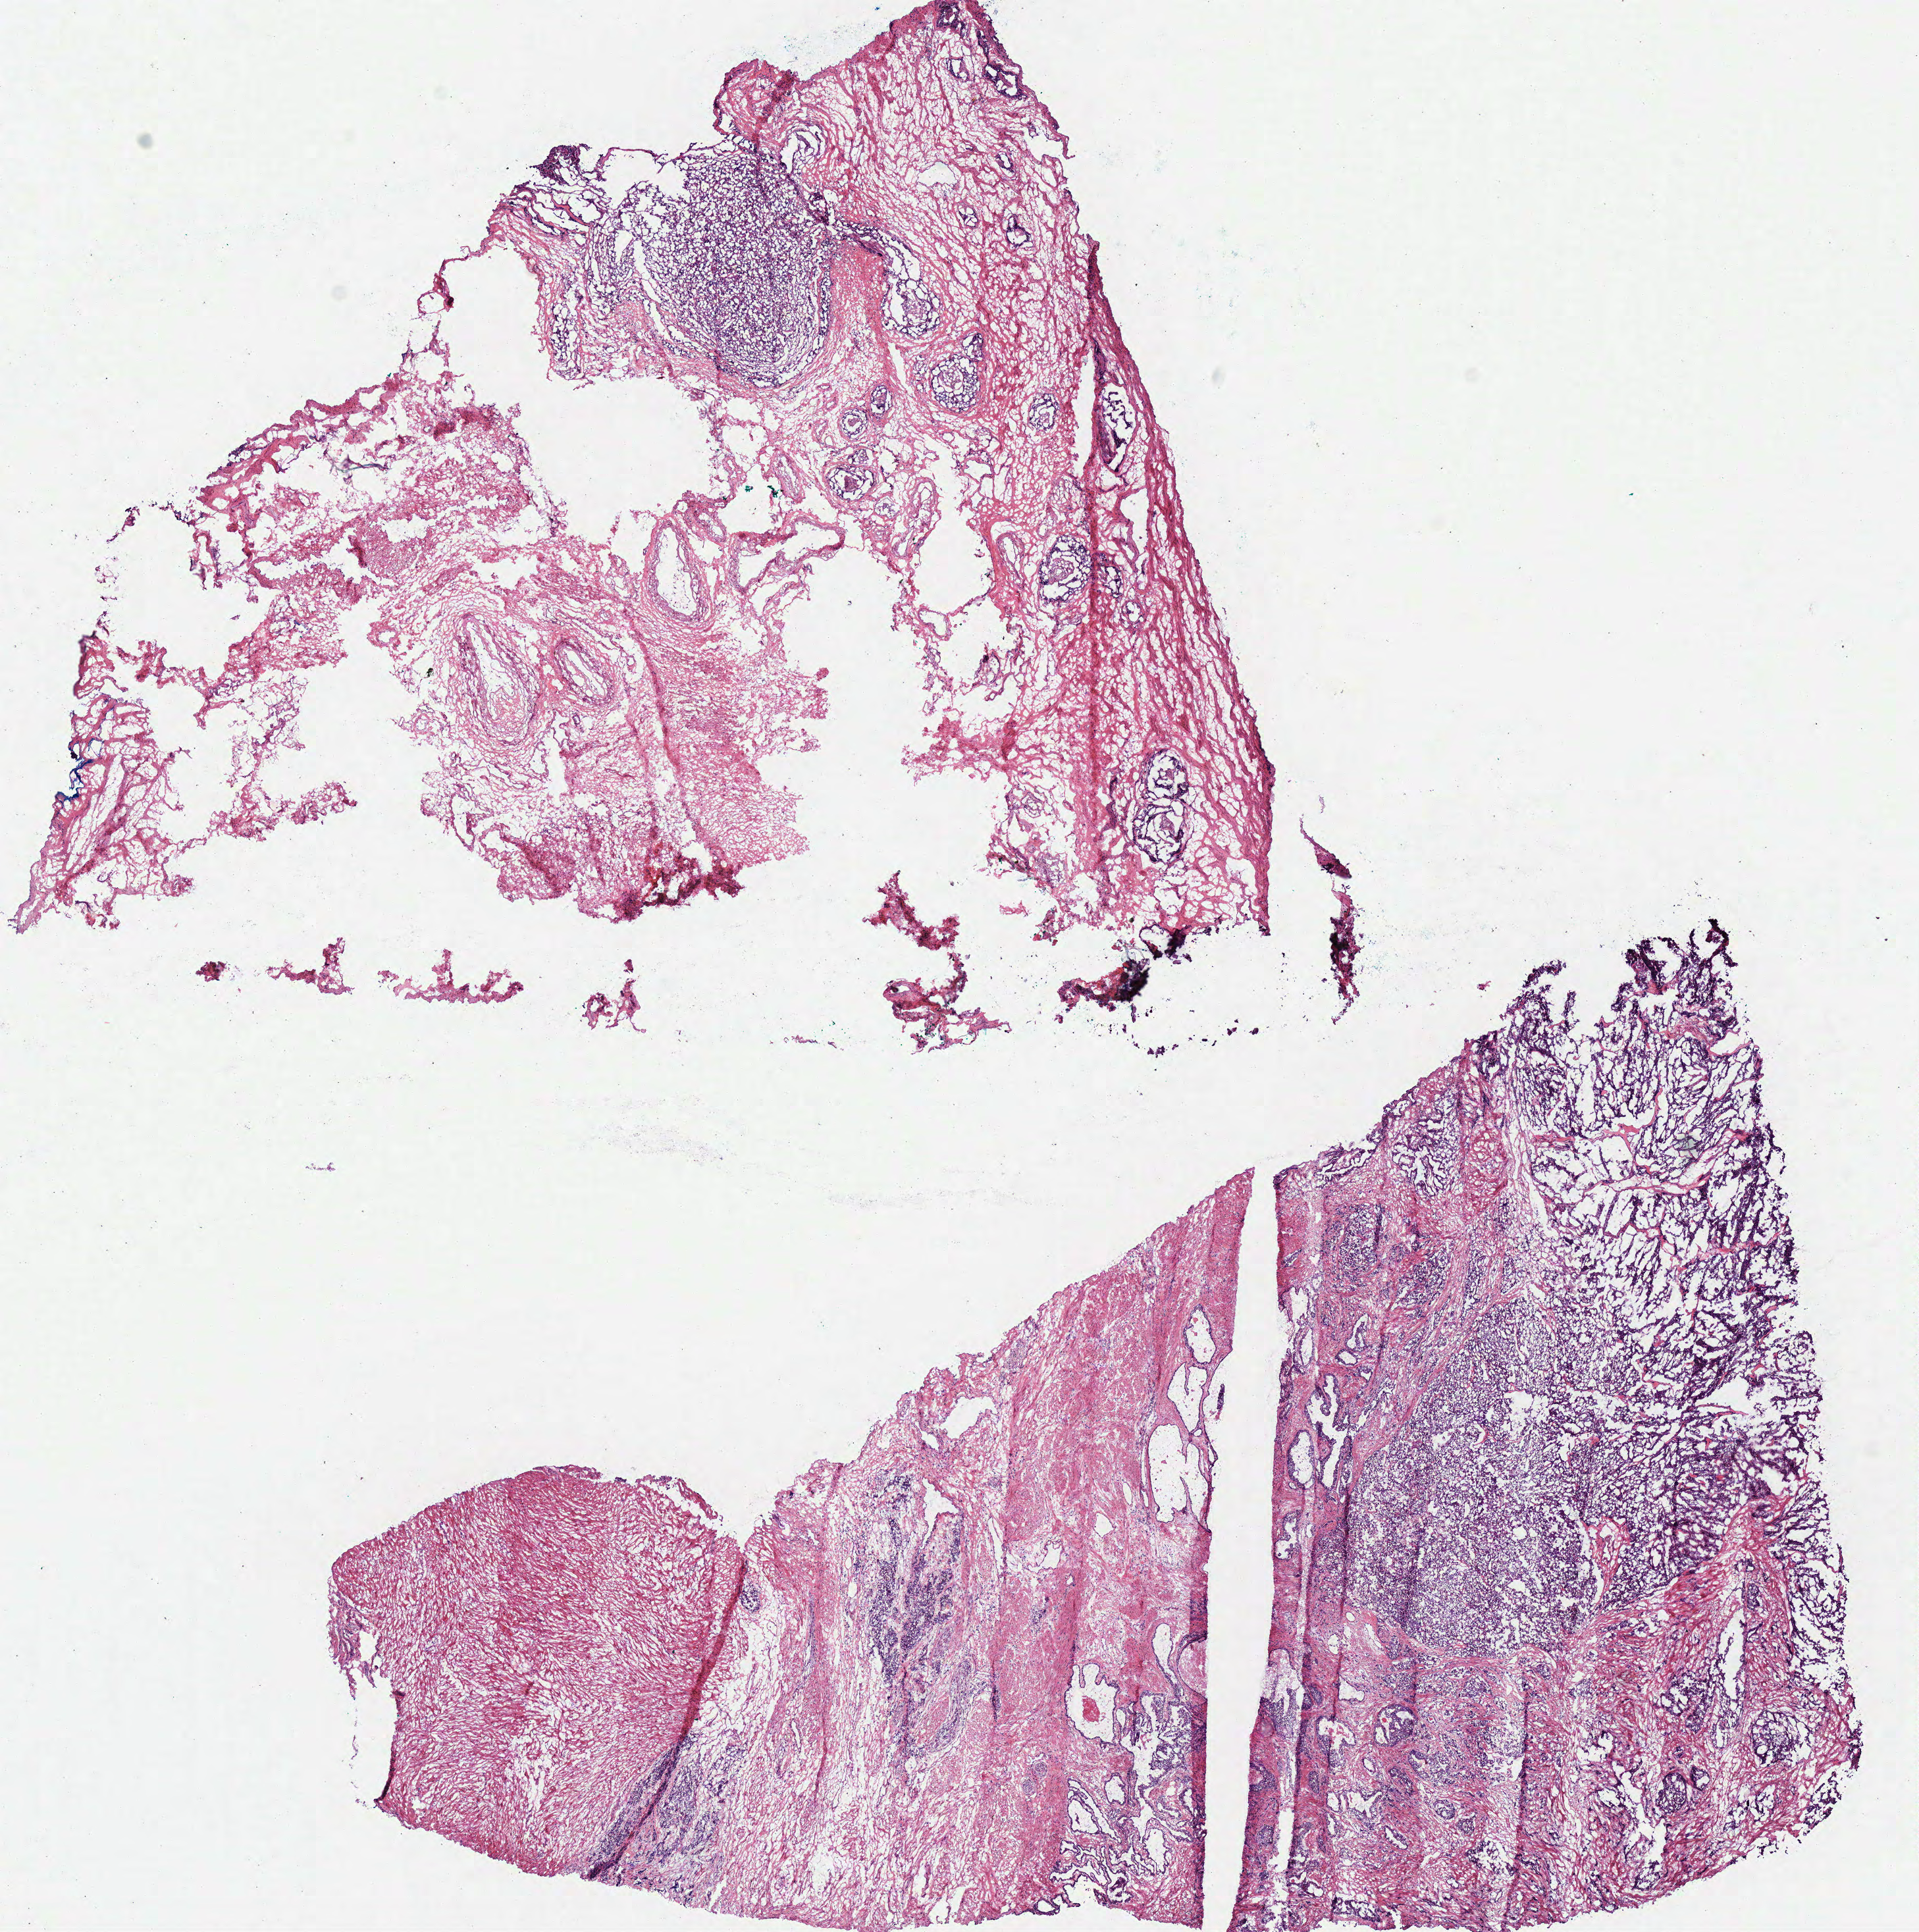
H&E-stained whole-slide image, a low-resolution overview of the entire scanned area, about 11.5 x 11.6 mm (slide scanned at 40x), frozen section from the top of the tissue portion, sample: primary tumour, prostate. Patient: male, age at initial diagnosis 62 years. Gleason score: 9 (4+5). Pathologist review of this section (percent, as recorded): tumour cells 40%, tumour nuclei 65%, normal cells 0%, stromal cells 58%, necrosis 2%.
Lymph nodes positive (case pathology): 0 of 9 examined. Laterality: bilateral. Diagnosis: Acinar cell carcinoma (prostate gland).